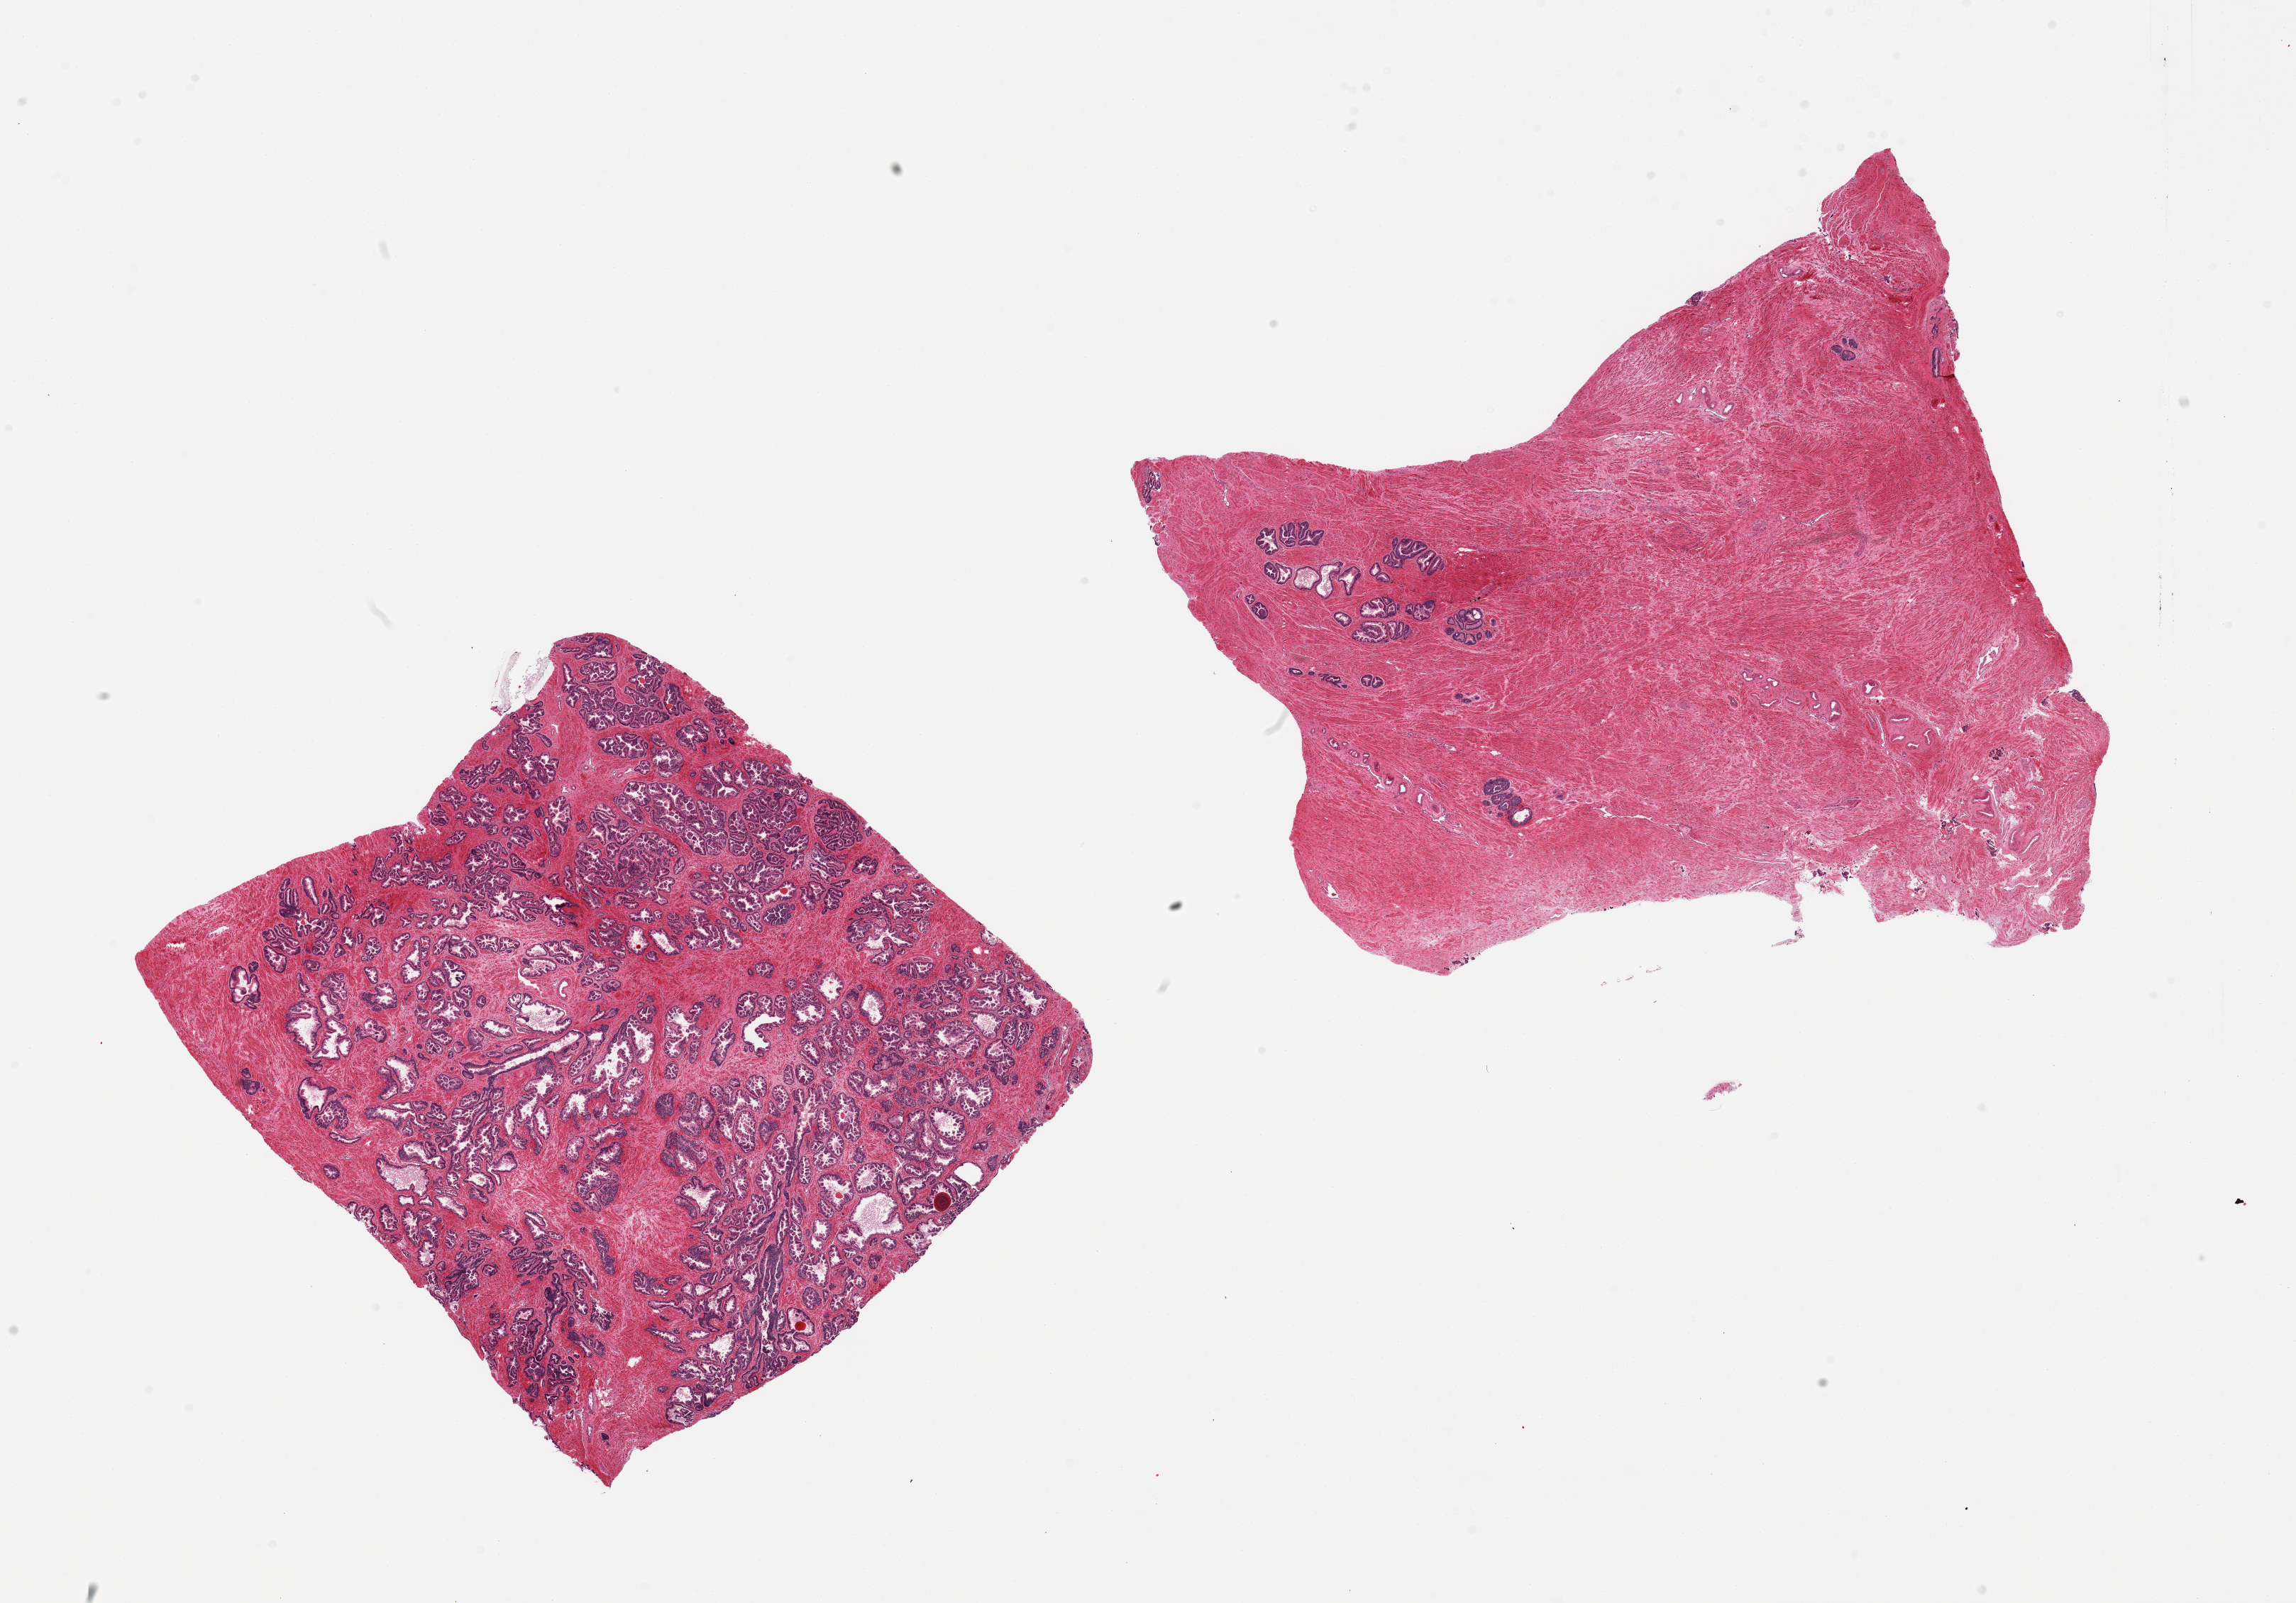
Whole-slide image, H&E stain — whole scanned area (about 25.6 x 17.9 mm, slide scanned at 20x) shown as a low-resolution overview, PAXgene-fixed, paraffin-embedded tissue, section of prostate (target tissue), tissue donor sample. Donor sex: male.
* reviewer comment on this tissue sample: 2 pieces; one piece is 50/50 stroma and glands, second is predominantly stroma with only focal representation of glands